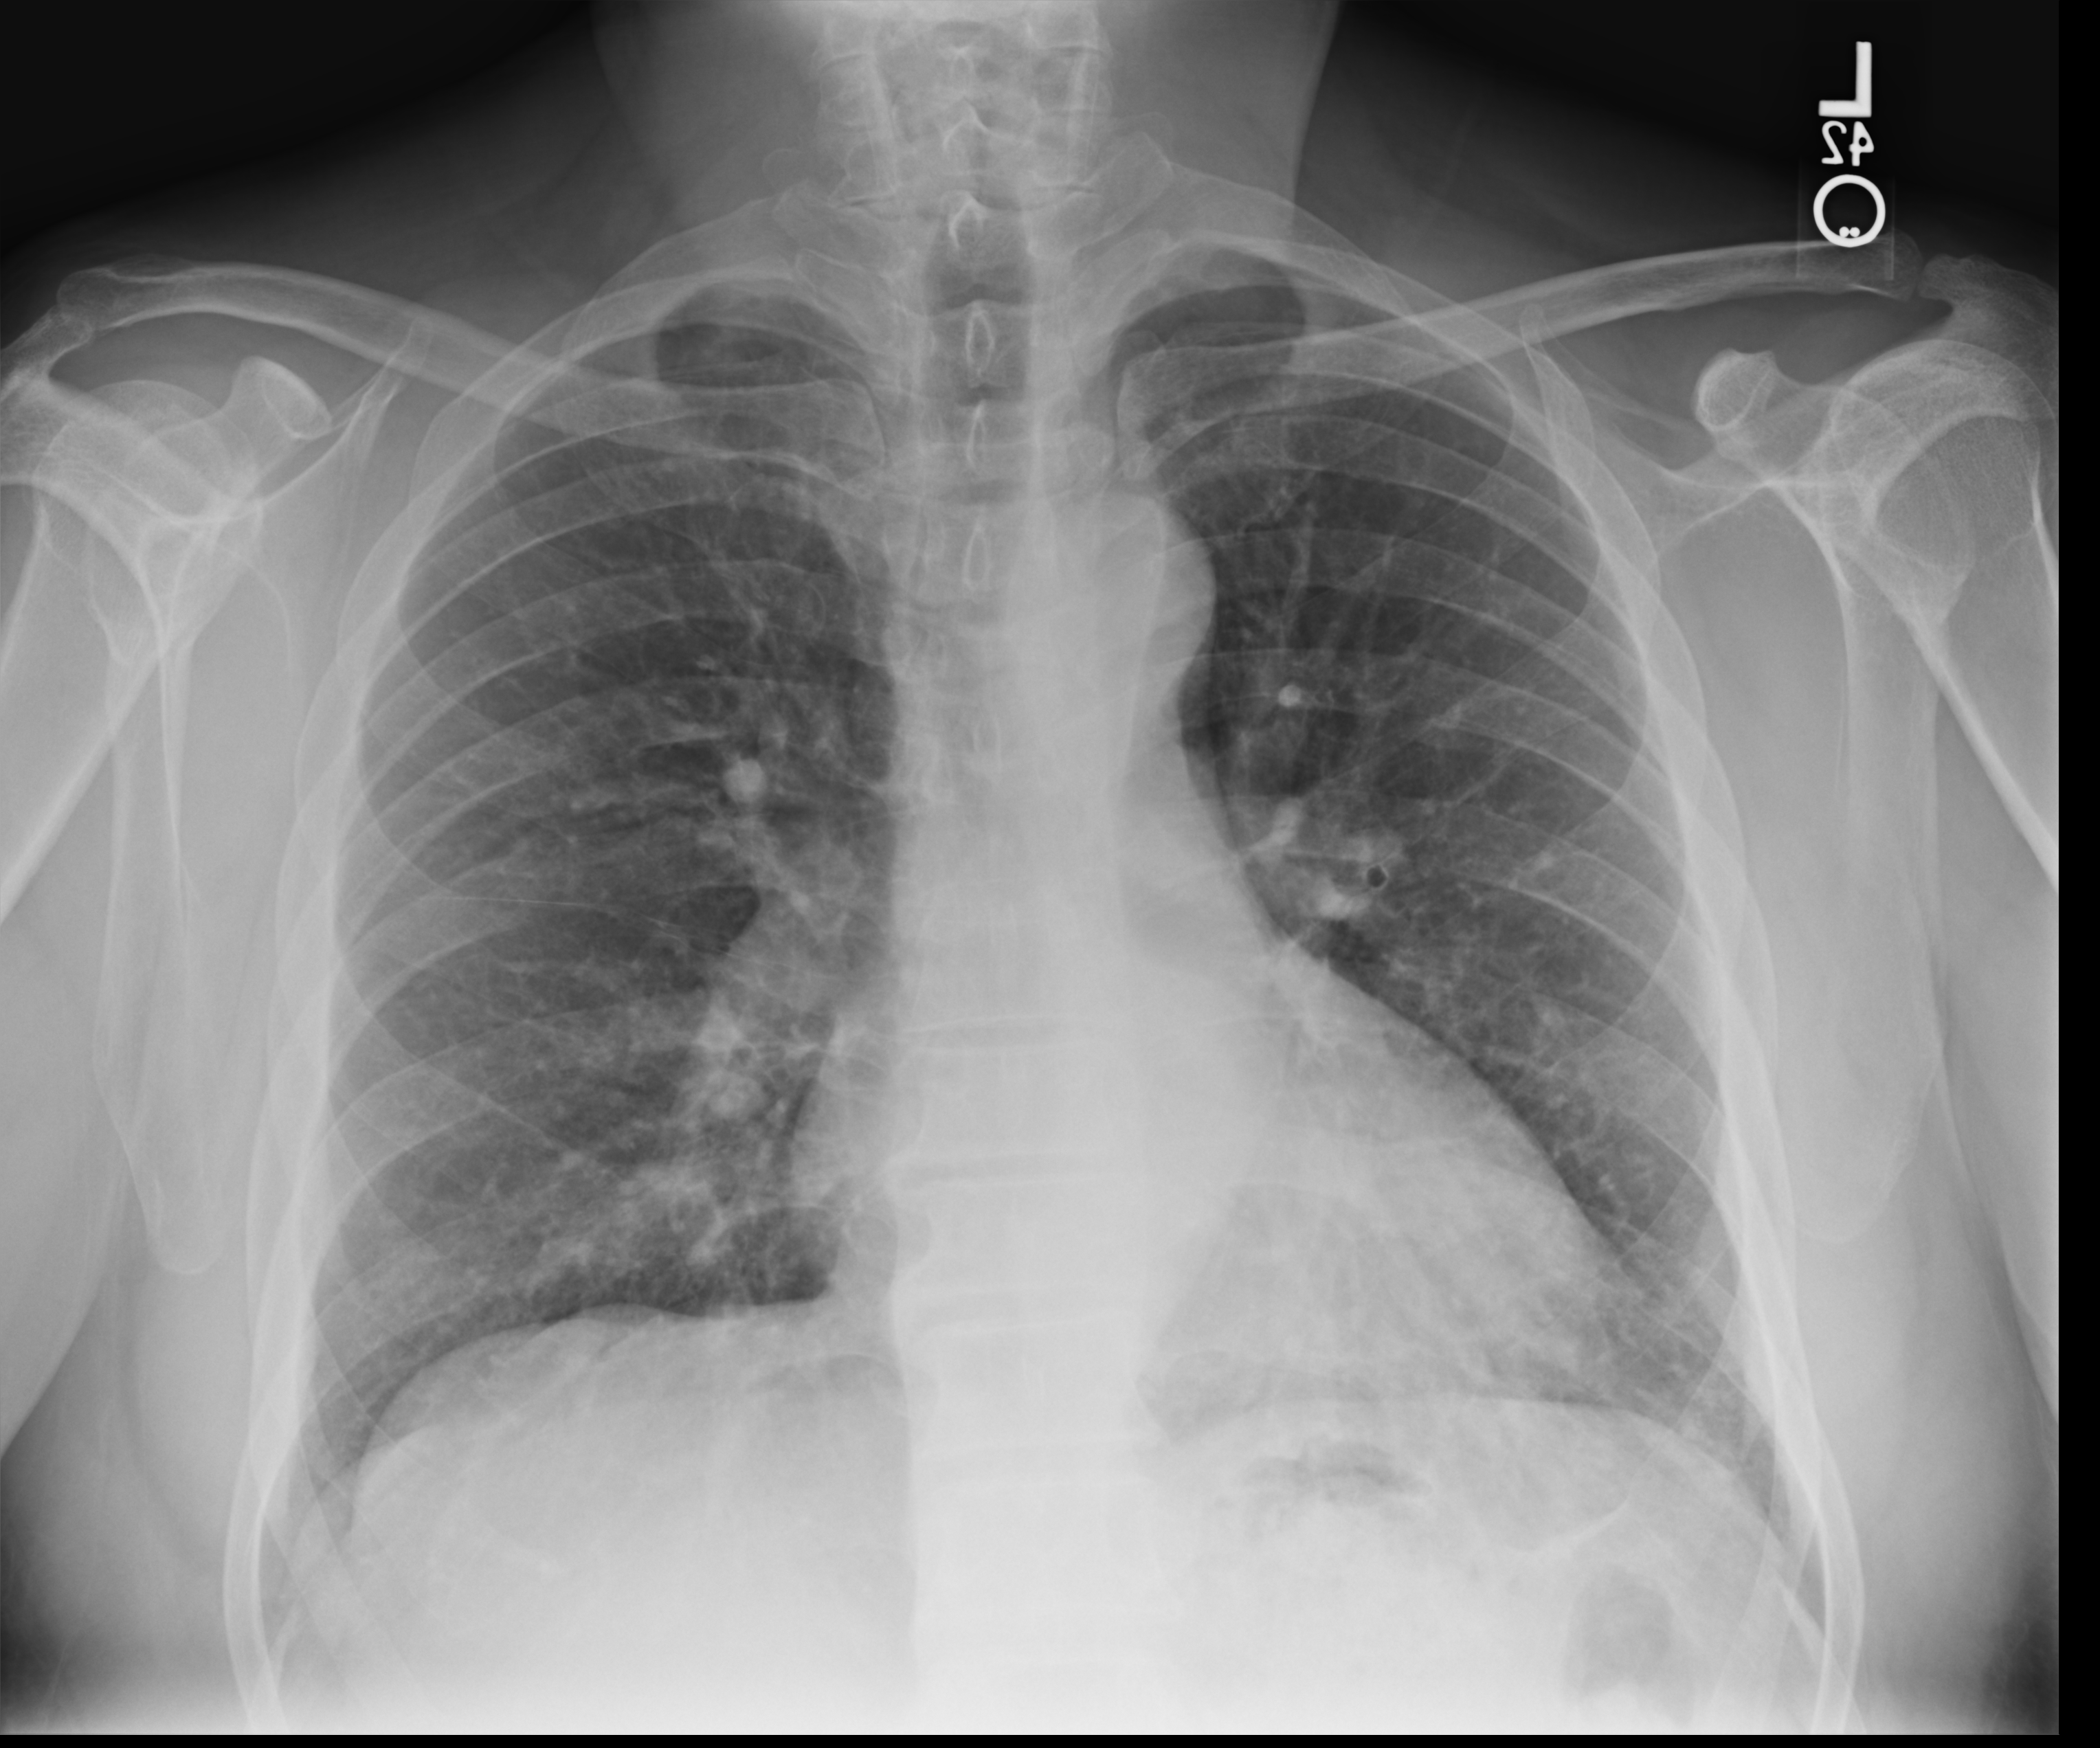
Chest radiograph (computed radiography). Male patient hospitalised with COVID-19, age 60–74 years.
Hospital-stay facts (about this admission, not read from this image; timing relative to this image not recorded): admitted to intensive care during this hospital stay: no; mechanically ventilated during this hospital stay: no.